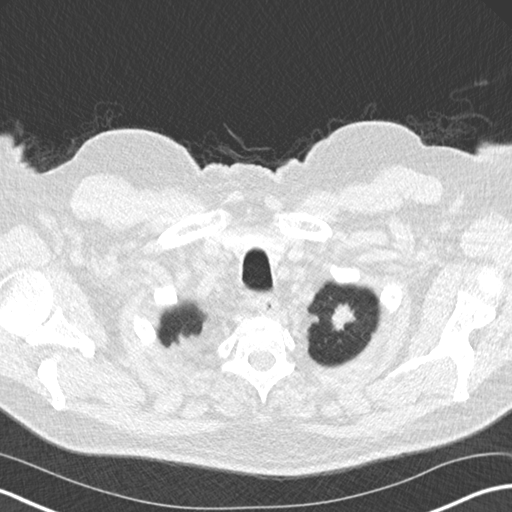
Low-dose screening chest CT, one axial slice; slice 156 of 175 in the series (ordered by position); lung window (W 1500 / L -600 HU); 2 mm slice thickness; 512 × 512 image matrix, field of view 351 × 351 mm.
Annotated regions visible in this slice (expert manual segmentation):
- lesion 1 (tumor, upper lobe of left lung): bounding box (x1, y1, x2, y2) in pixels: (332, 304, 356, 330)